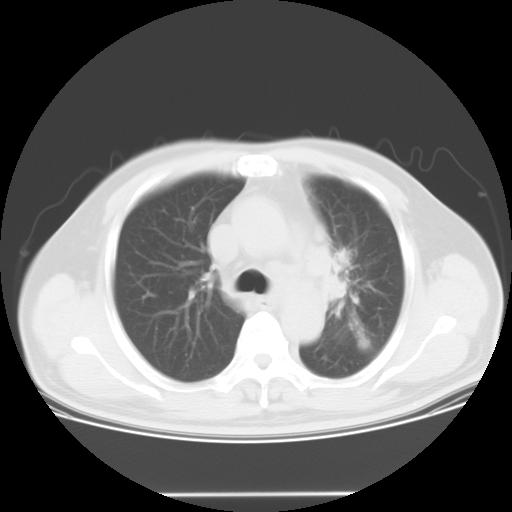
Chest CT, one axial slice. Reconstruction kernel STANDARD. 120 kVp. Lung window (W 1500 / L -600 HU). 10 mm slice thickness. 512 × 512 image matrix, field of view 398 × 398 mm. Patient: male, 61 years. Case-level facts recorded for this patient, not image findings: clinical TNM (as recorded): T3 N1 M1; histopathological grade: G3.
Structures marked on this image (bounding box drawn by a radiologist):
- lung tumour (recorded histology: small cell carcinoma): bounding box [x1, y1, x2, y2] px = [323, 227, 375, 333]